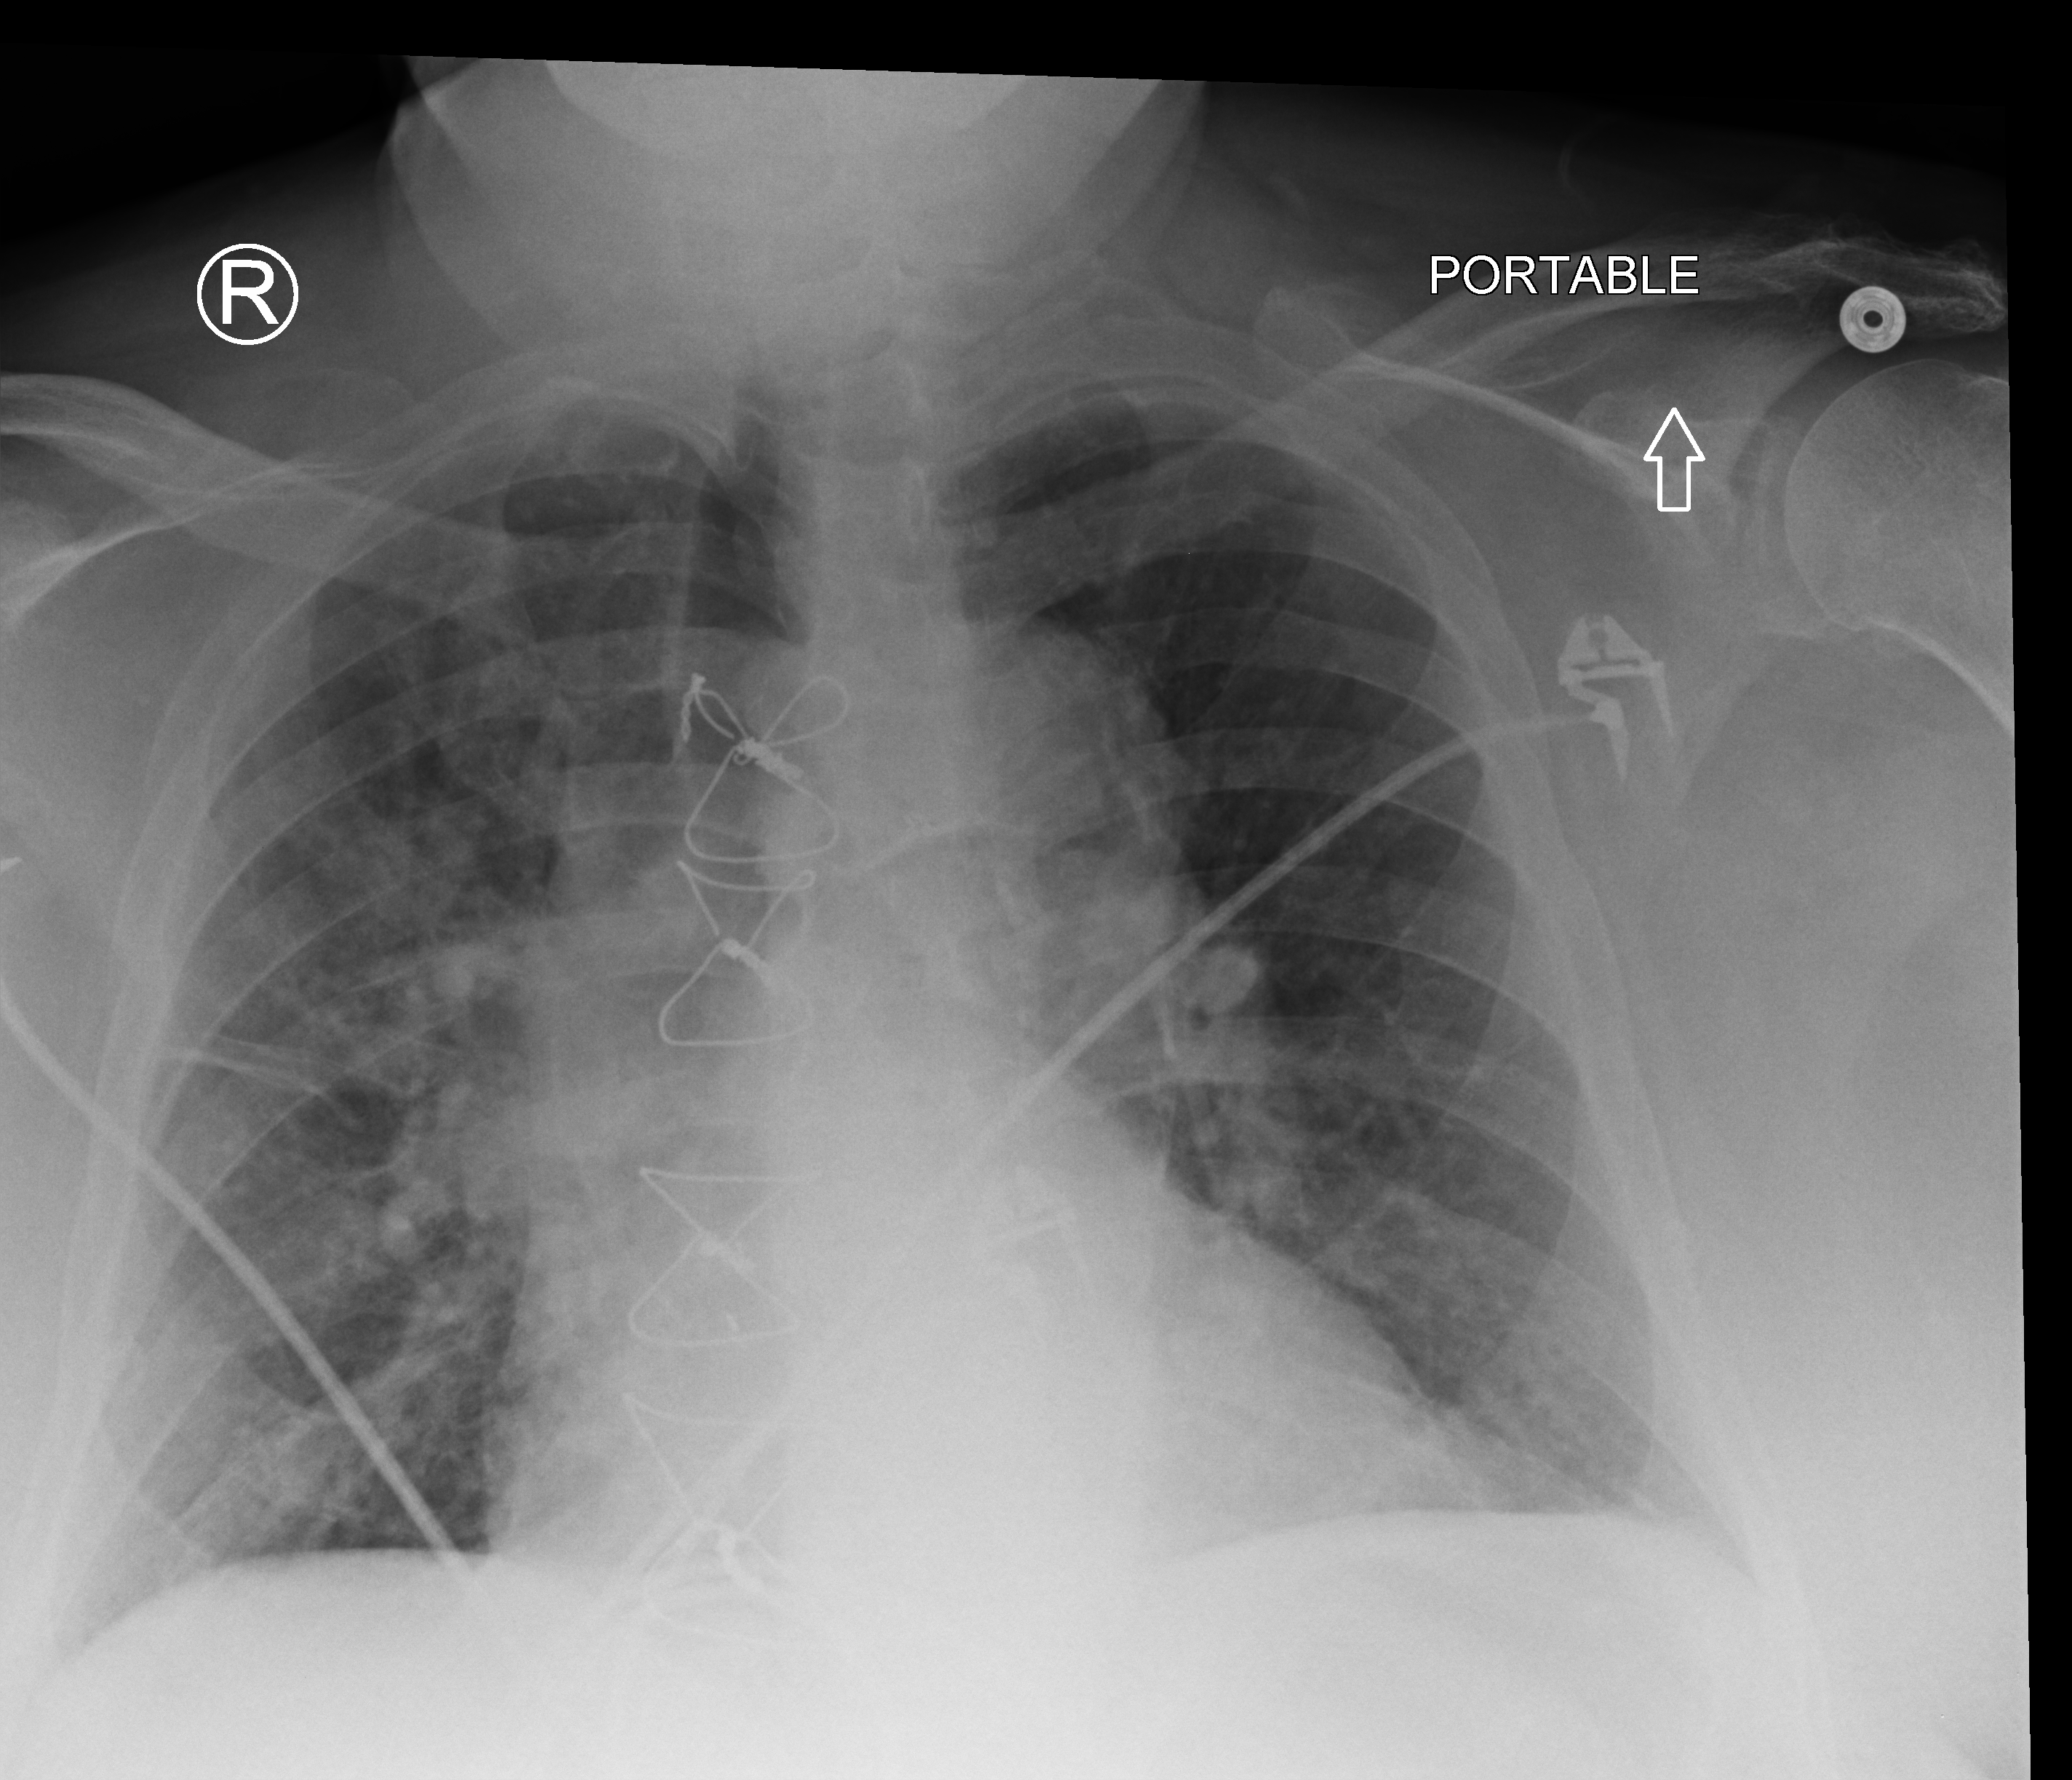
Chest X-ray (portable); anteroposterior (AP) projection. Patient hospitalised with COVID-19; male, aged 75–90 years.
From the hospital-stay record, not from the radiograph (when in the stay this image was taken is not recorded): mechanically ventilated during this hospital stay: no; smoking status (admission record): never.